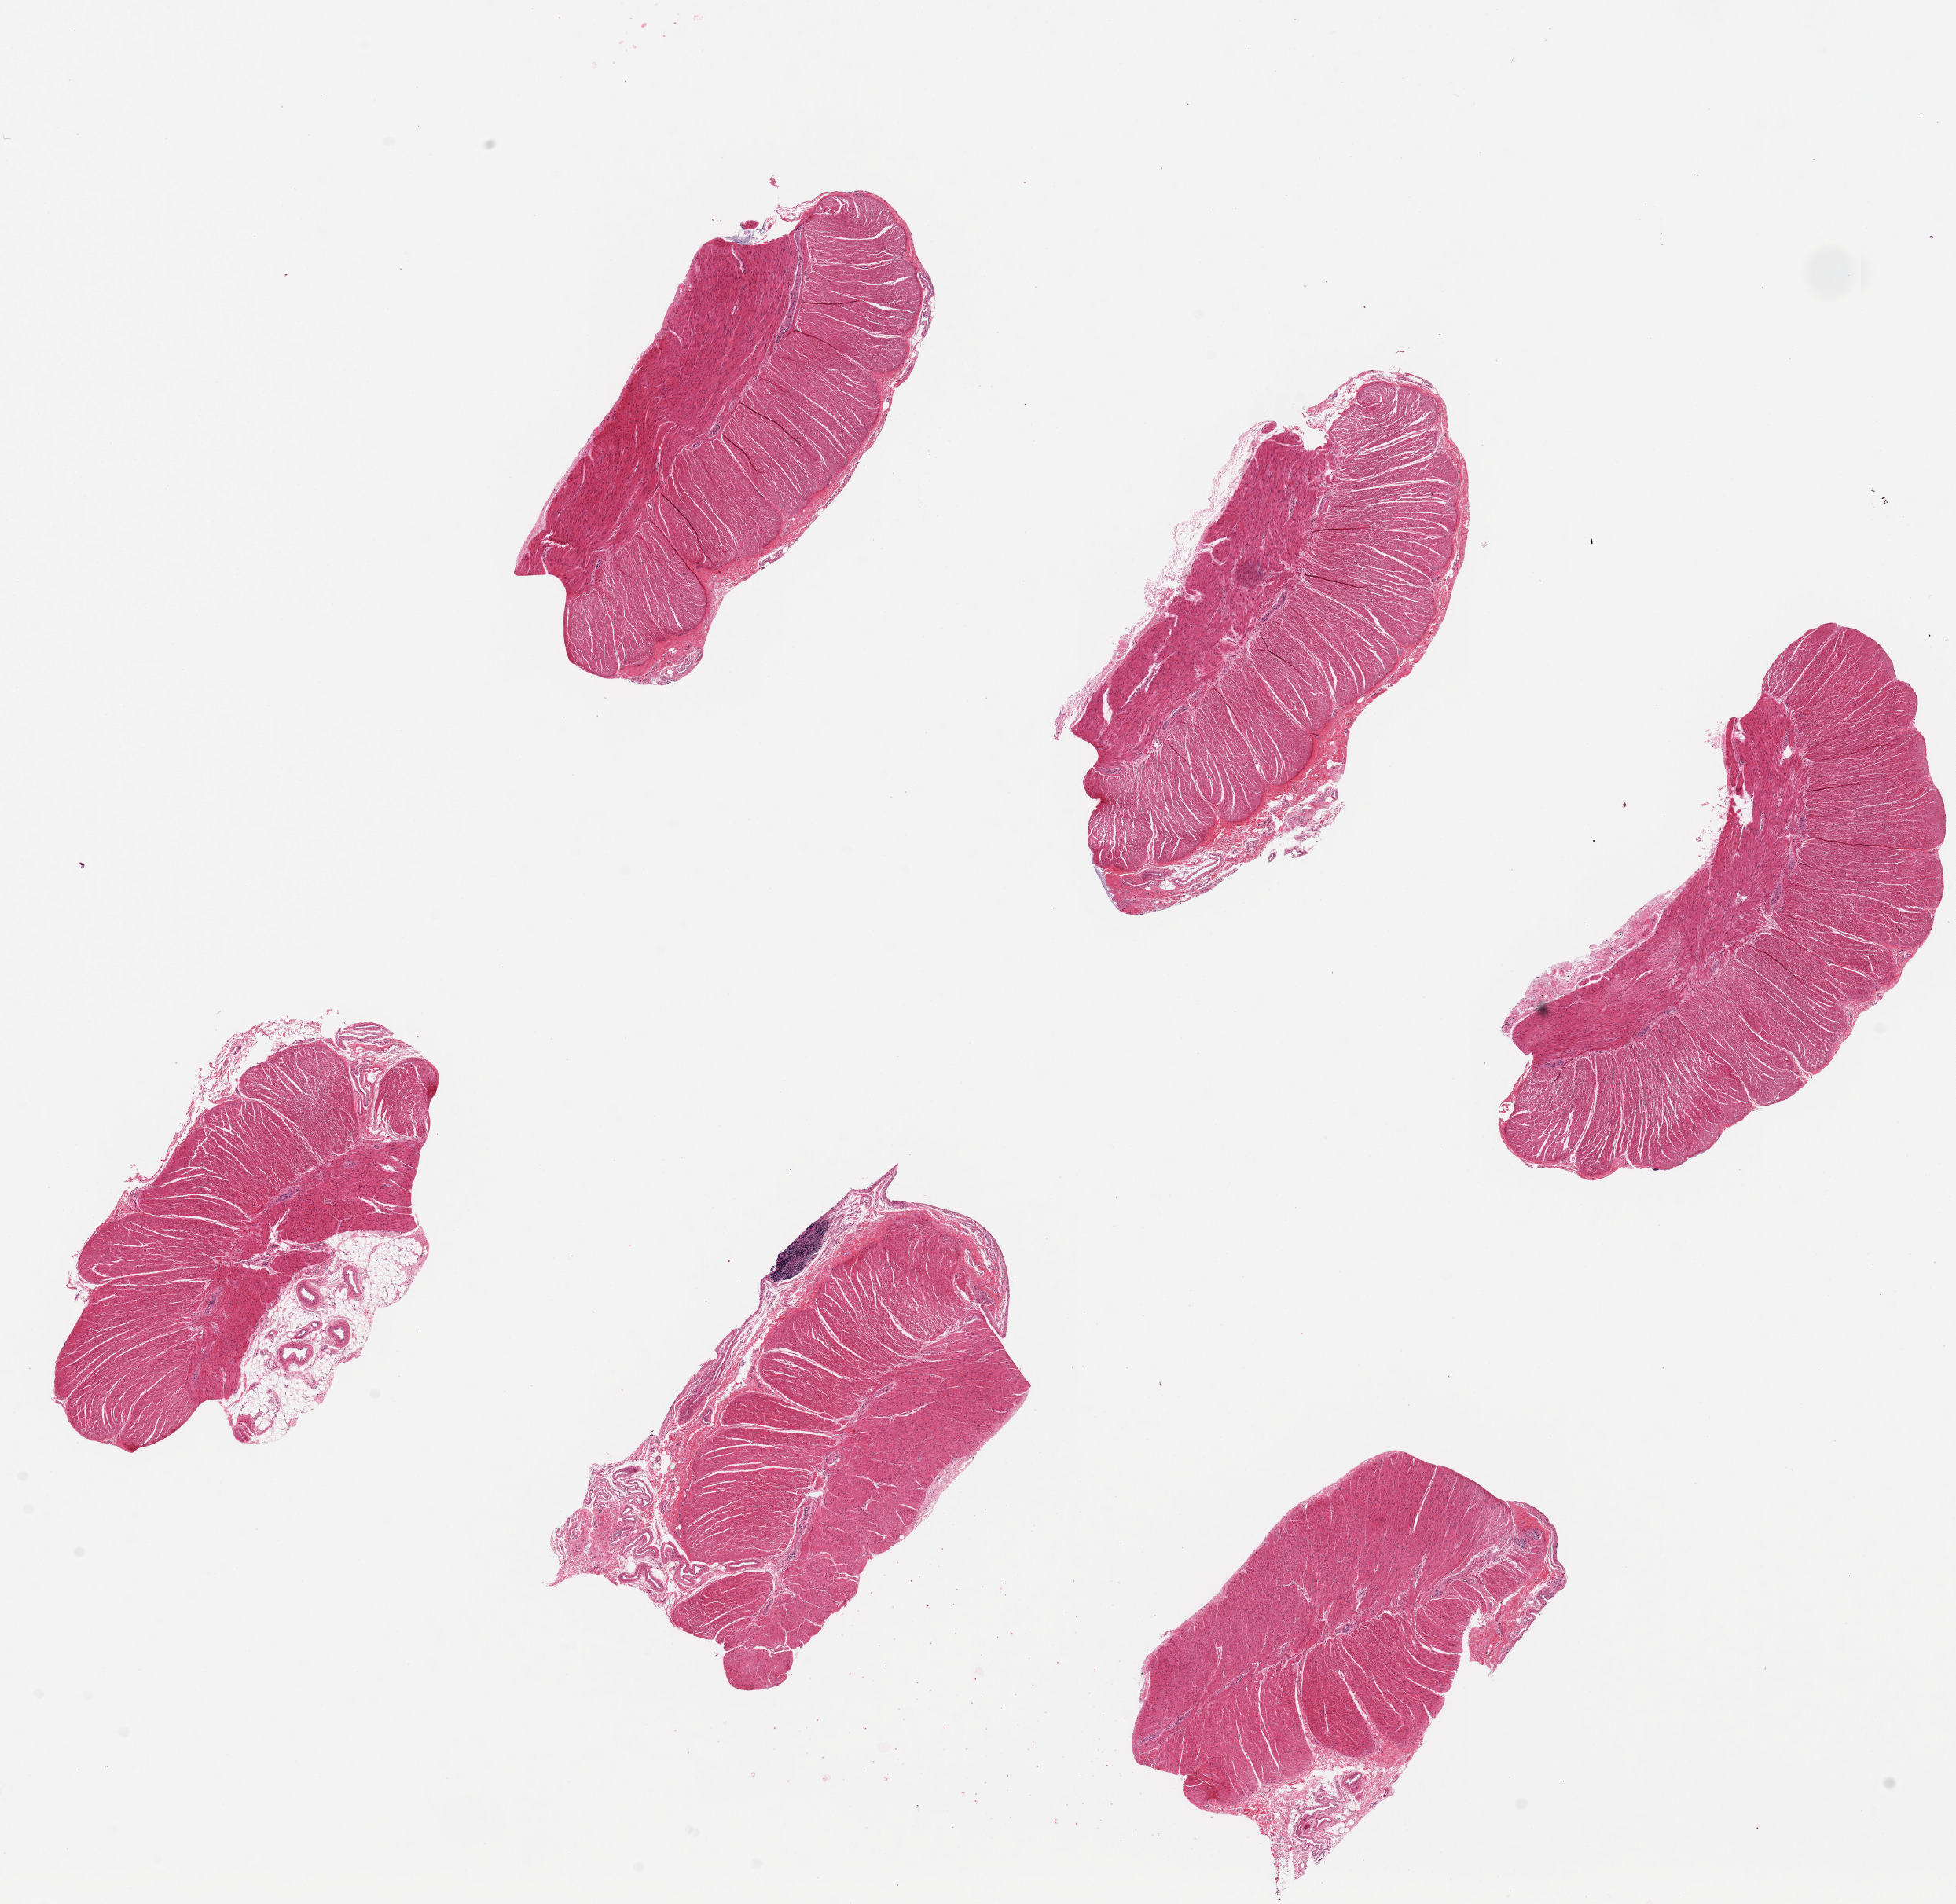
Whole-slide image, haematoxylin and eosin stain, shown as a low-resolution overview of the whole scanned area (about 19.7 x 19.2 mm); PAXgene-fixed paraffin-embedded (PFPE) section; section of sigmoid colon (target tissue); tissue donor sample.
- review note (as recorded): 6 pieces, up to 6x3mm; 1 of 6 has pericolonic adipose; others have well trimmed muscularis